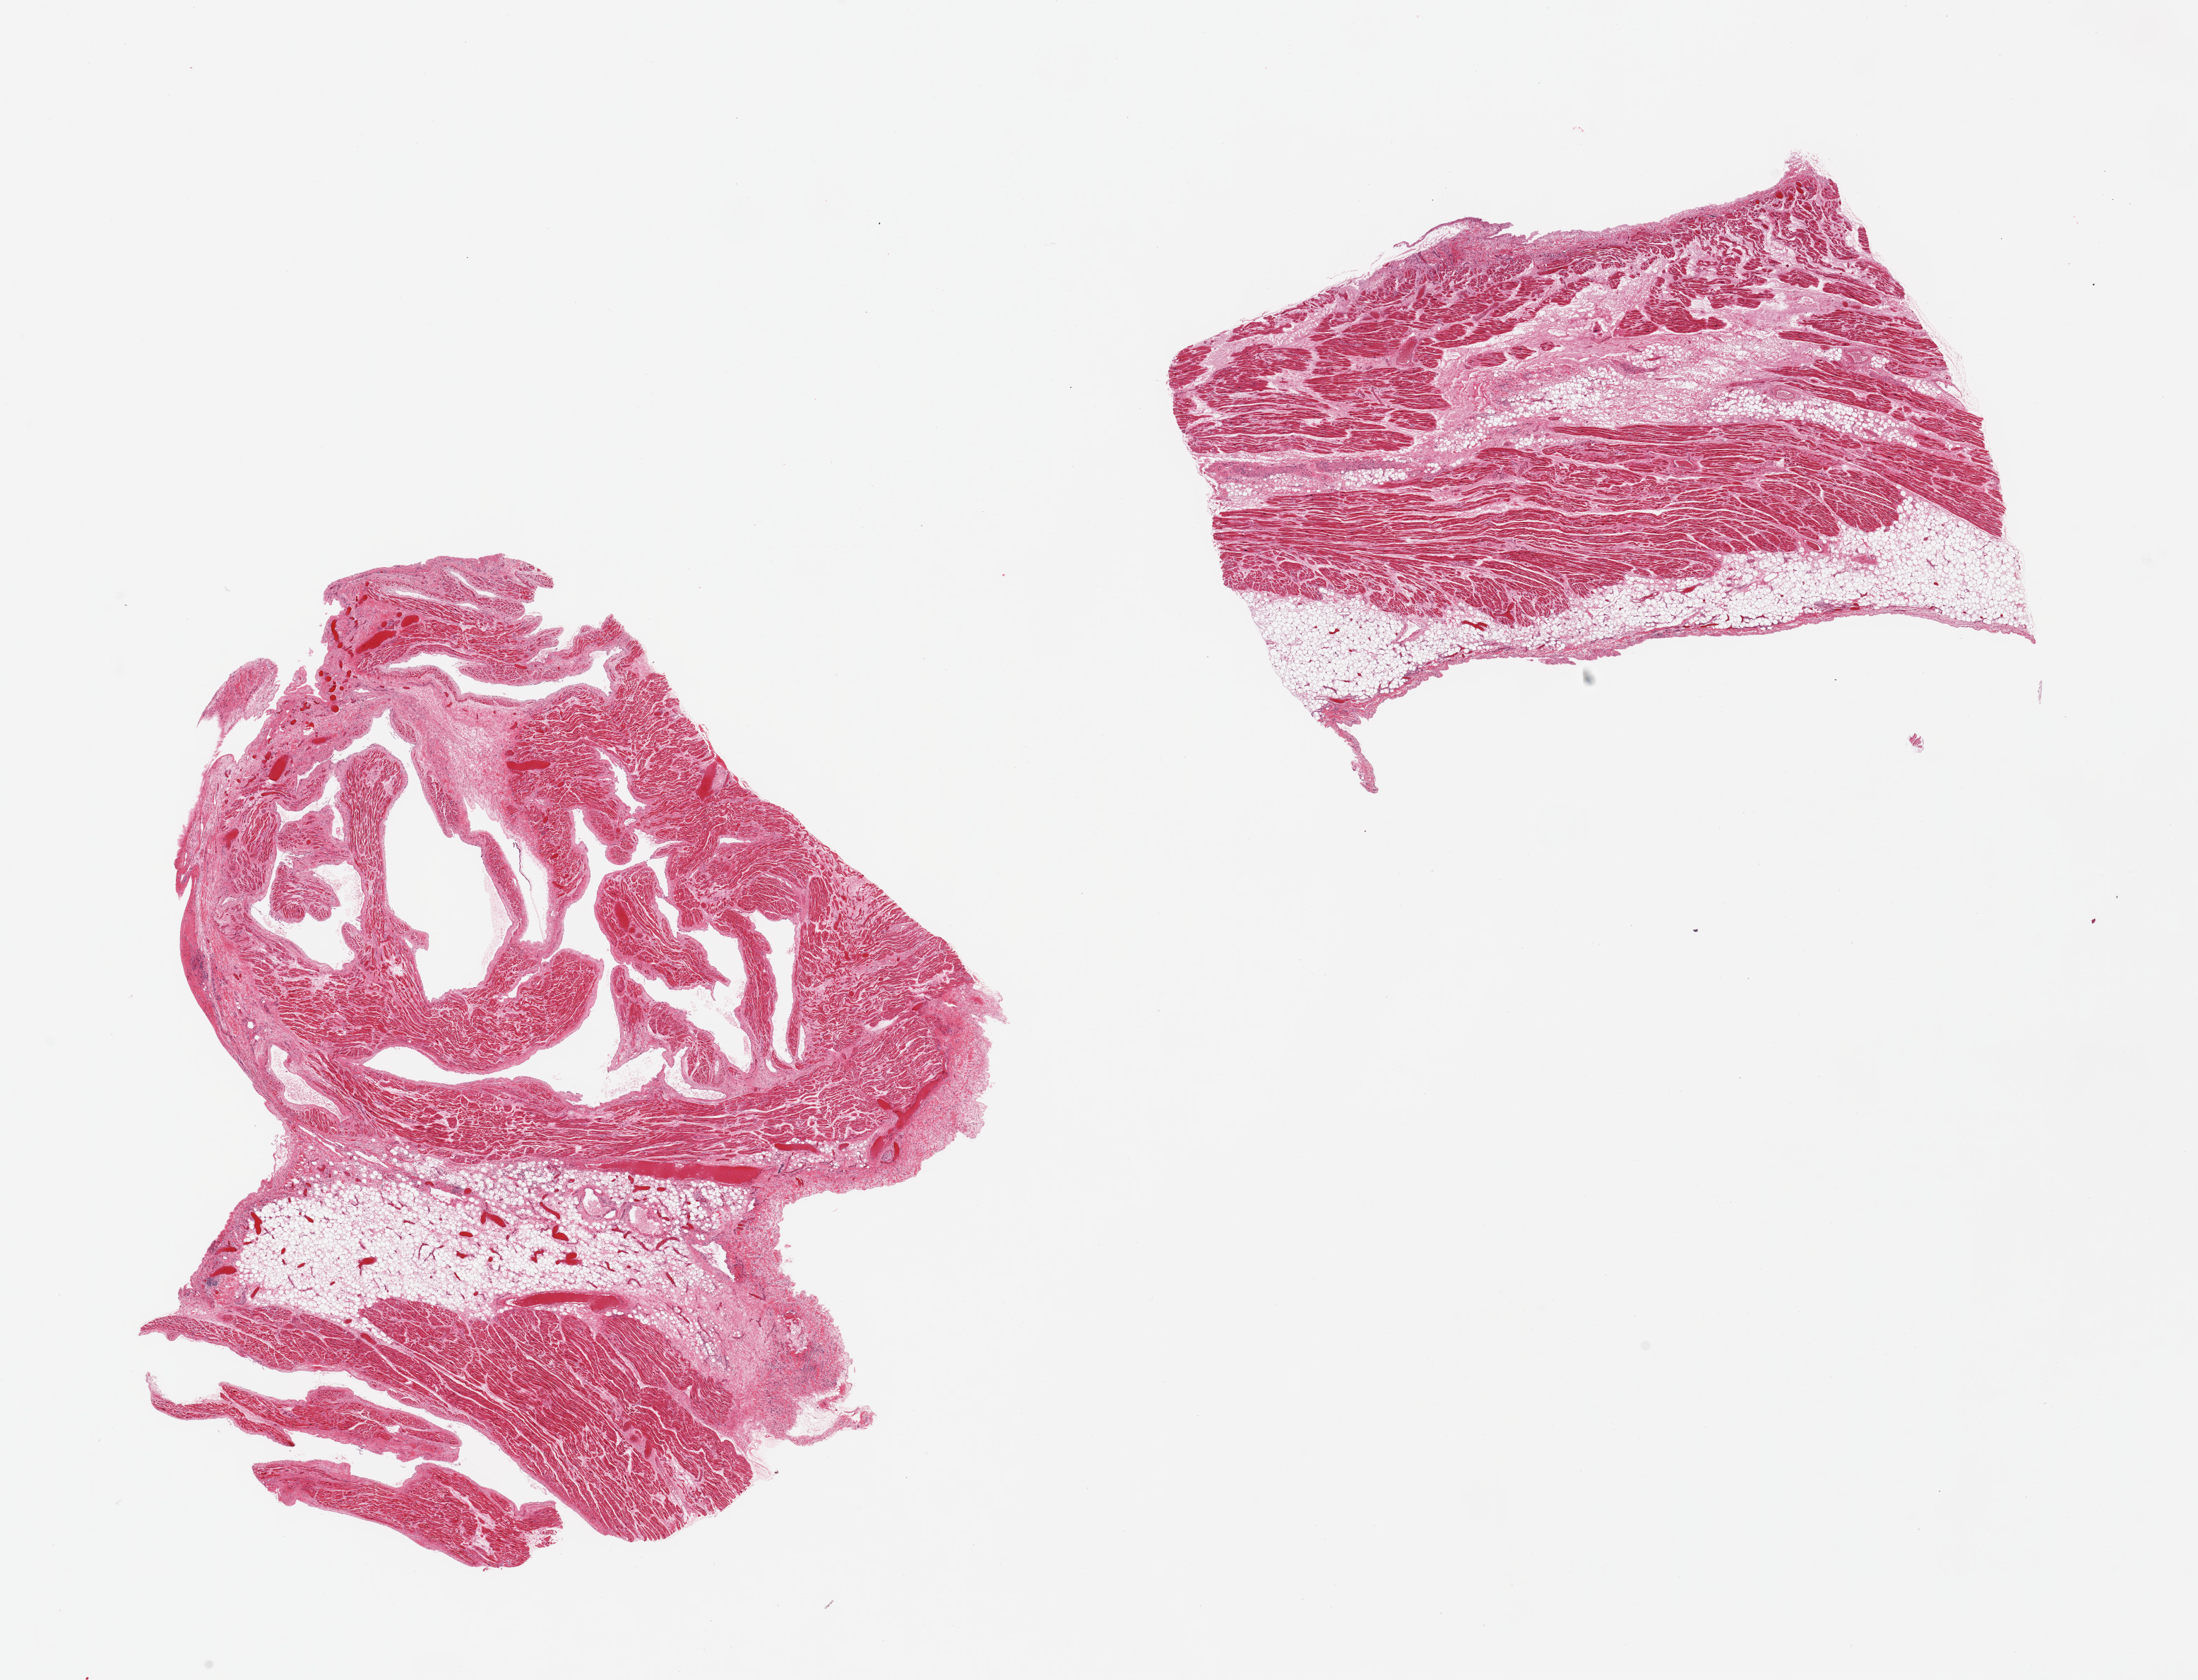
Haematoxylin and eosin whole-slide image, a low-resolution overview of the entire scanned area, about 24.6 x 18.8 mm (from a 20x scan). PAXgene-fixed, paraffin-embedded tissue. Target tissue: auricular appendage. Tissue donor sample.
- pathologist's review note for this sample: 2 pieces; ~30% is fat/fibrous, focal chronic inflammation